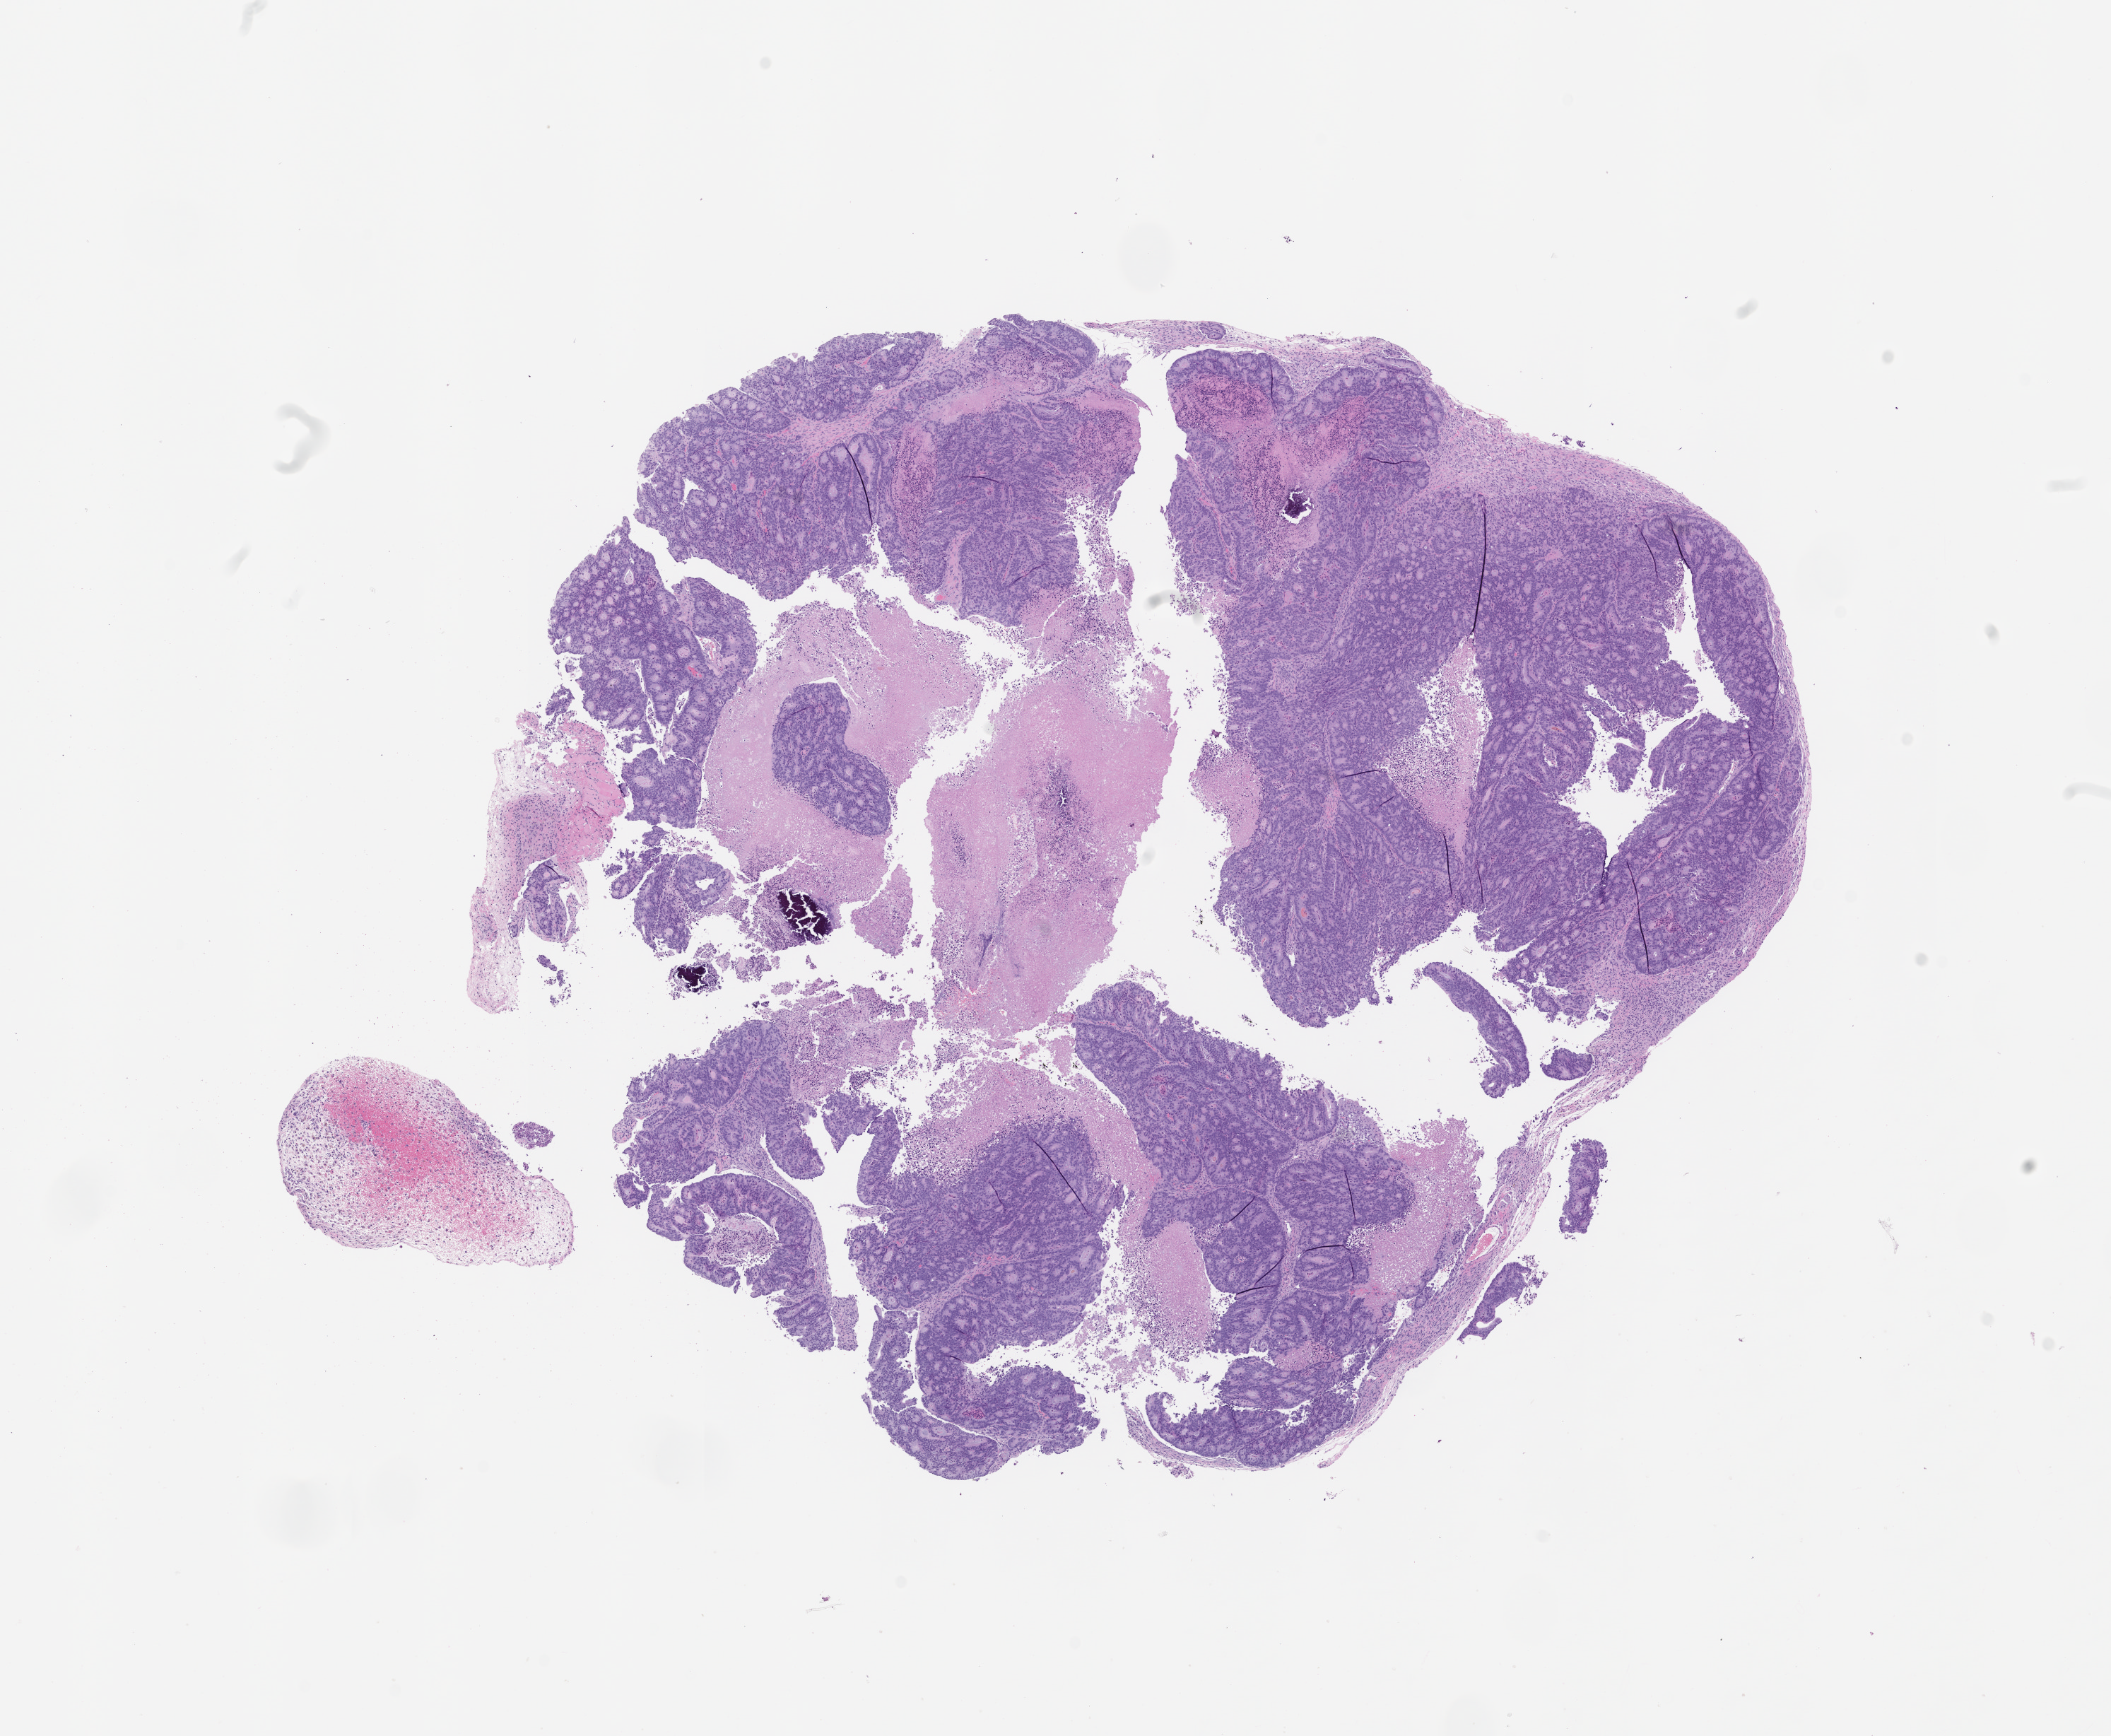
Whole-slide image, H&E: patient-derived xenograft (human tumor grown in a mouse), passage 1 — low-resolution overview of the scanned area, about 12.0 x 9.8 mm; formalin-fixed, paraffin-embedded (FFPE) tissue; tumor site category: colon.
Originating patient diagnosis: Colon Adenocarcinoma.